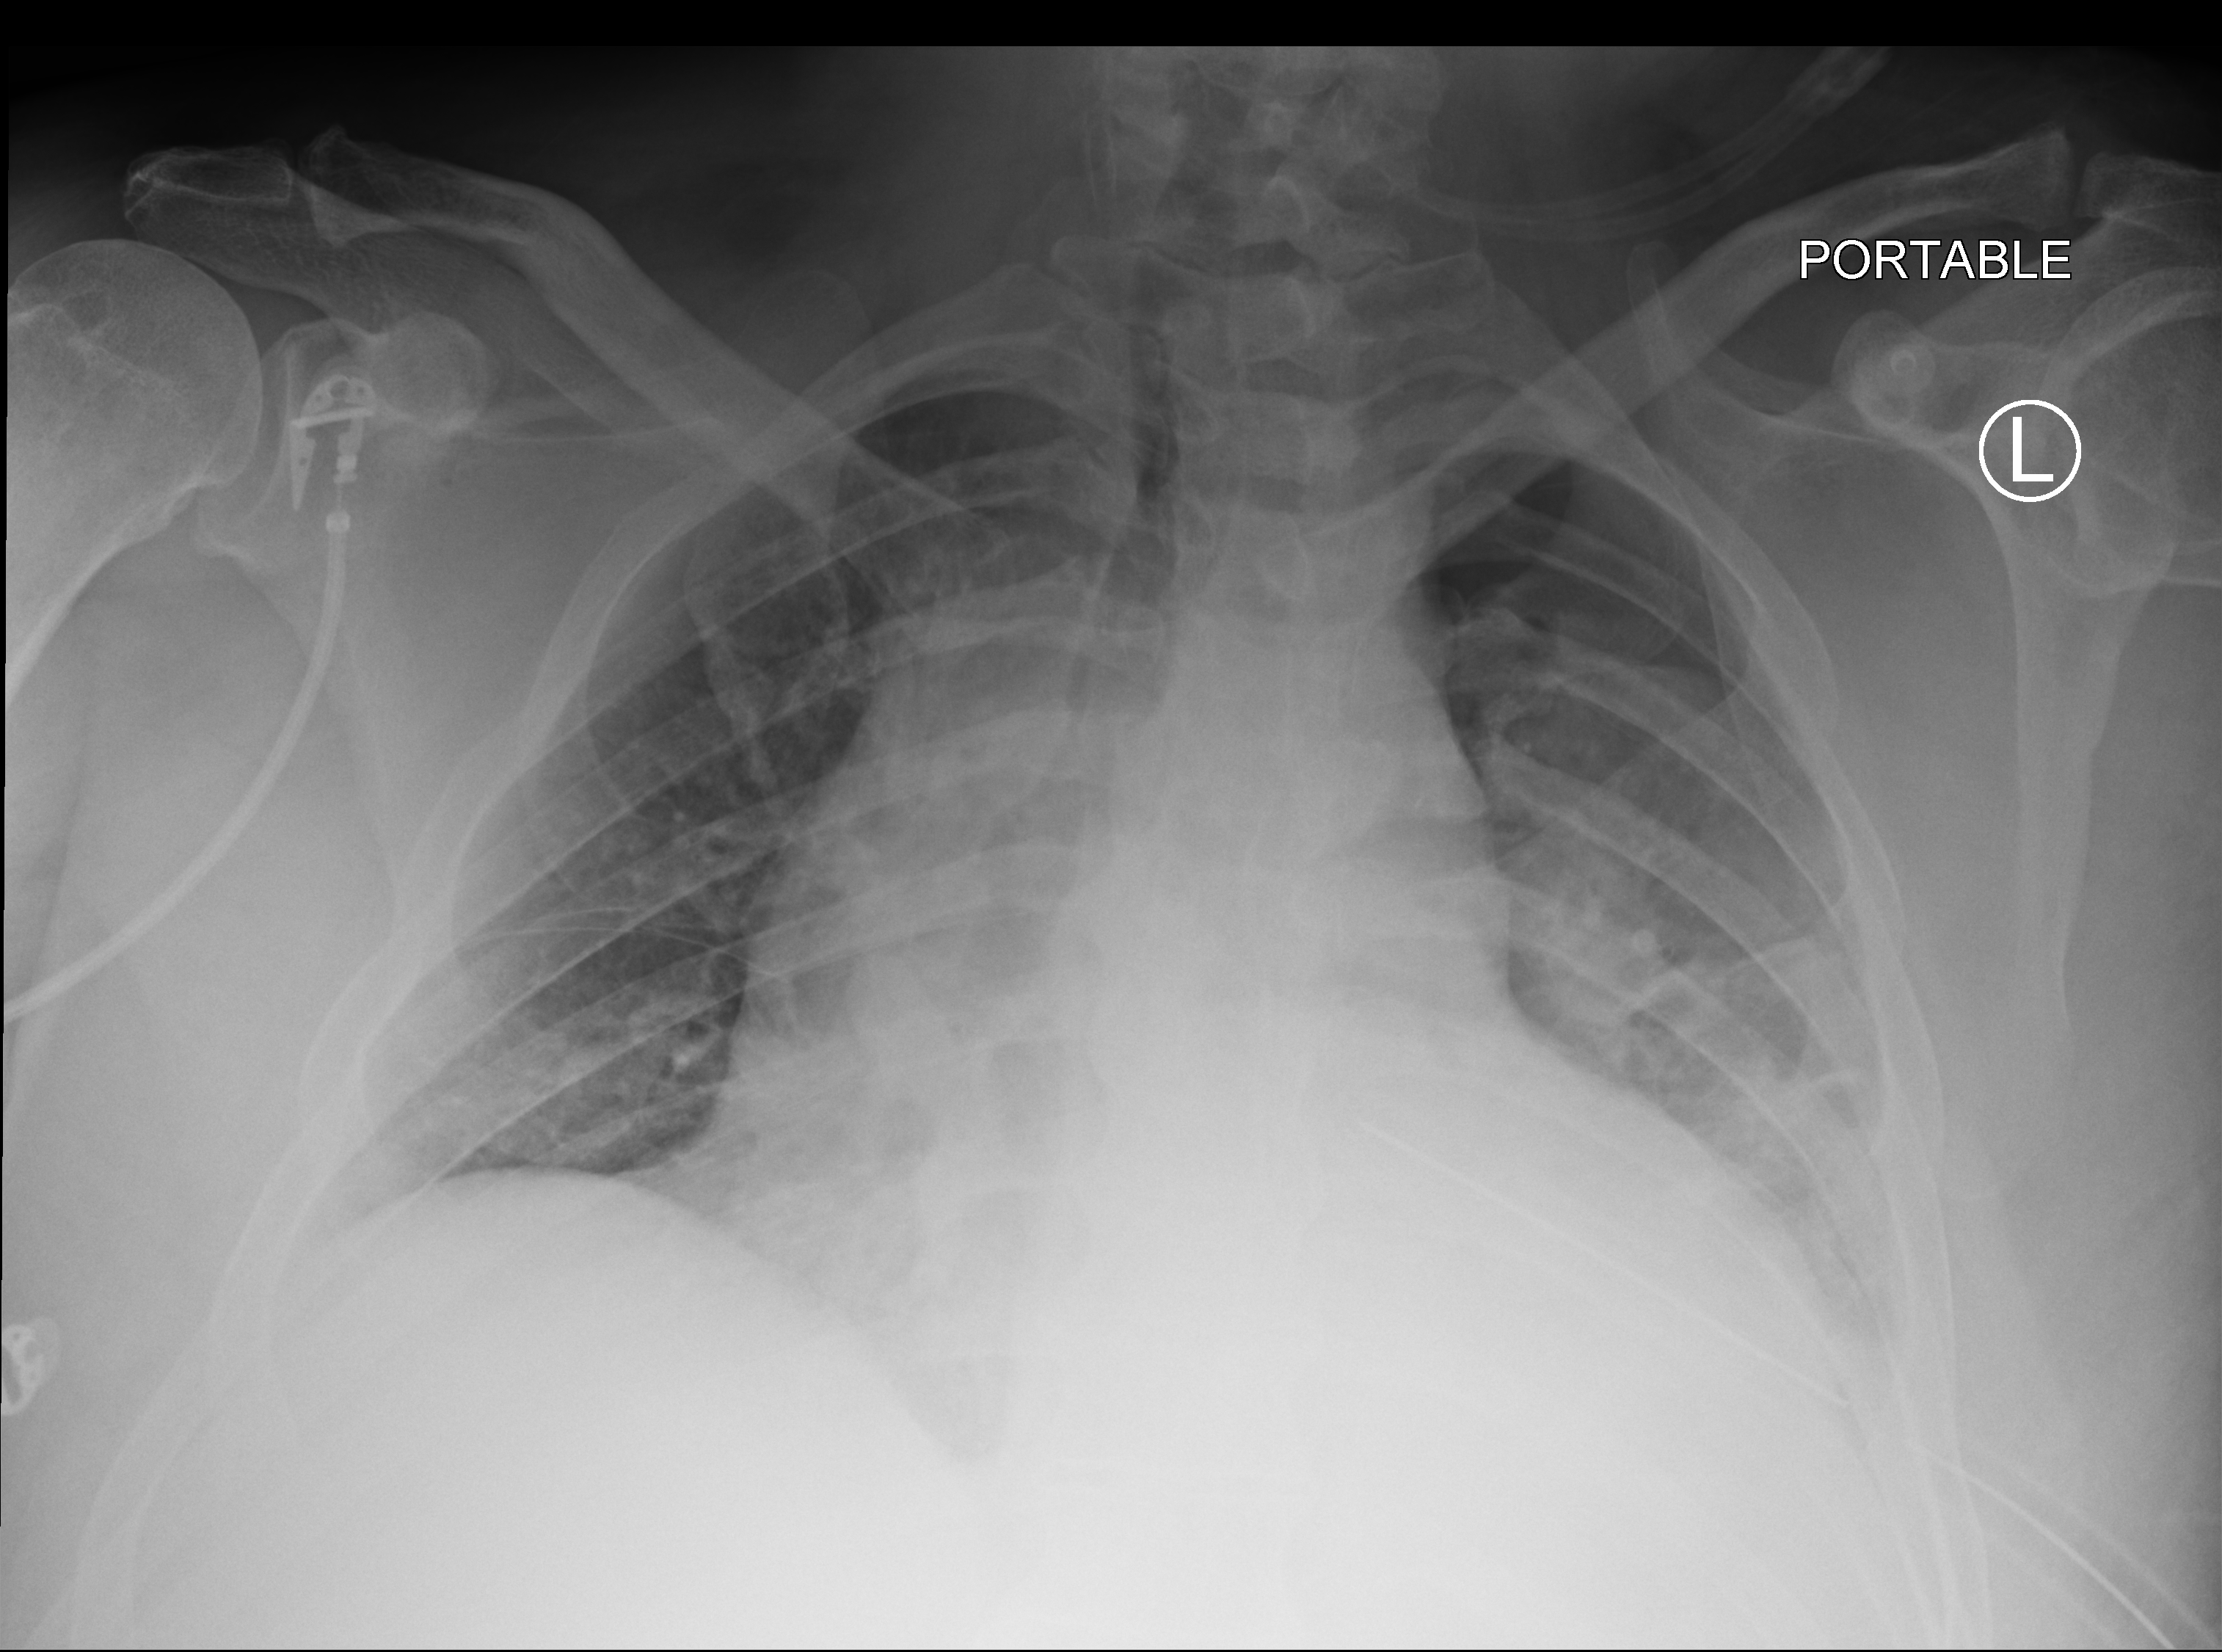
Bedside chest radiograph (computed radiography); anteroposterior (AP) projection. Male patient hospitalised with COVID-19, age 18–59 years.
From the hospital-stay record, not from the radiograph (when in the stay this image was taken is not recorded):
- mechanically ventilated during this hospital stay: no